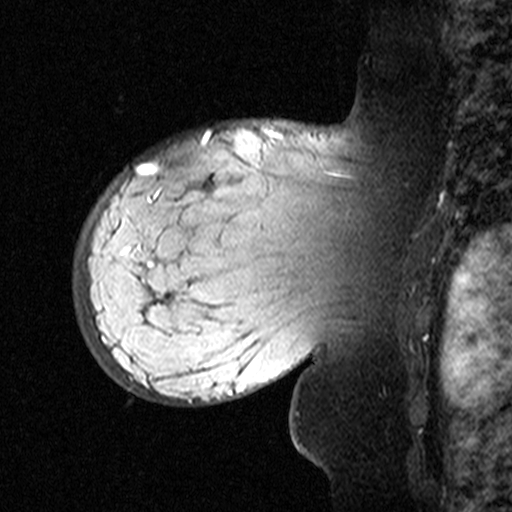
Breast MRI (dynamic contrast-enhanced), one sagittal slice. Position 35 of 44 along the scan axis. Dynamic contrast-enhanced study with each time point stored as its own series, time point 2 of 3 at this slice position (early post-contrast, ordered by acquisition time). 1.5 T. TE 4.5 ms, TR 11 ms. 3 mm slice thickness. 512 × 512 image matrix, field of view 200 × 200 mm. Female patient, age 53 years. From the clinical record (not read from this slice): setting: breast cancer imaged before/during neoadjuvant chemotherapy; receptor status: HR-positive, HER2-negative.
Structures marked on this image (semi-automatically segmented with operator editing):
- analysis volume of interest (the breast-tissue region the enhancement analysis was run in; not a lesion): box from (x=76, y=140) to (x=311, y=353) px
- tumour enhancement mask (voxels above the 90 % enhancement threshold inside the analysis volume of interest): (x=148, y=171)–(x=156, y=267)